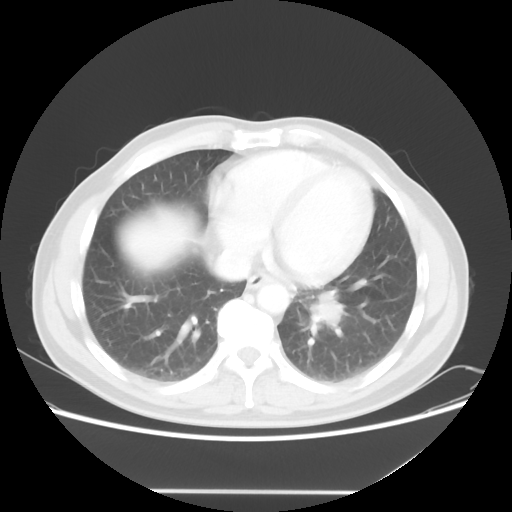
Chest CT, one axial slice. Position 19 of 56 along the scan axis. Lung window (W 1500 / L -600 HU). 5 mm slice thickness. 512 × 512 image matrix, field of view 385 × 385 mm. Male patient, age 61 years. Case-level facts recorded for this patient, not image findings: clinical TNM (as recorded): T1c N0 M0; histopathological grade: G3.
Structures marked on this image (bounding box drawn by a radiologist):
- lung tumour (recorded histology: adenocarcinoma): box from (x=295, y=282) to (x=358, y=338) px